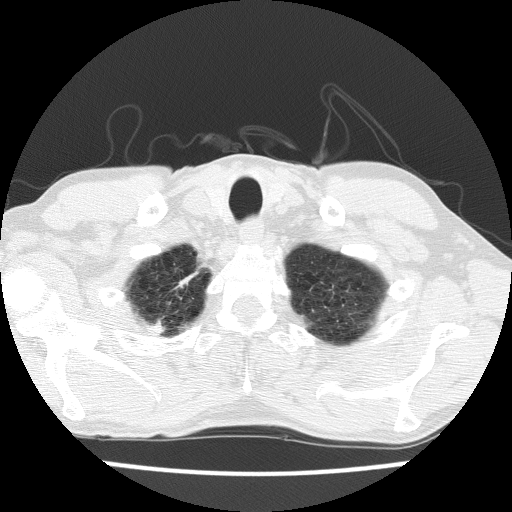
Axial slice from a low-dose chest CT screening exam; second annual screen; lung window (W 1500 / L -600 HU); 2 mm slice thickness; lung (sharp) reconstruction kernel (FC51); 512 × 512 image matrix, field of view 326 × 326 mm. Male, age 63 years at enrolment. Current smoker at enrolment.
Expert-annotated lung lesion, bounding box [x1, y1, x2, y2] px = [137, 264, 210, 334]. Screening reader's record for this exam: no non-calcified nodule ≥4 mm recorded.